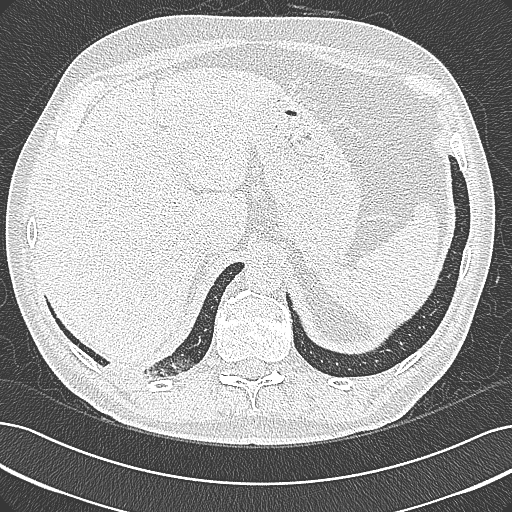
Low-dose screening chest CT, axial slice, baseline screening round, lung window (W 1500 / L -600 HU), lung (sharp) reconstruction kernel (B80f), slice 268 of 355 in the series, 512 × 512 image matrix, field of view 362 × 362 mm. Male participant, aged 68 years at enrolment. Former smoker at enrolment.
Expert-annotated lung lesion, box from (x=92, y=335) to (x=199, y=395) px. No non-calcified nodule or mass ≥4 mm was recorded by the screening reader at this exam. Later outcome: lung cancer diagnosed 154 days after this screen — mucinous adenocarcinoma, right lower lobe, well differentiated (G1), stage IB (AJCC 6th edition), 50 mm at pathology.